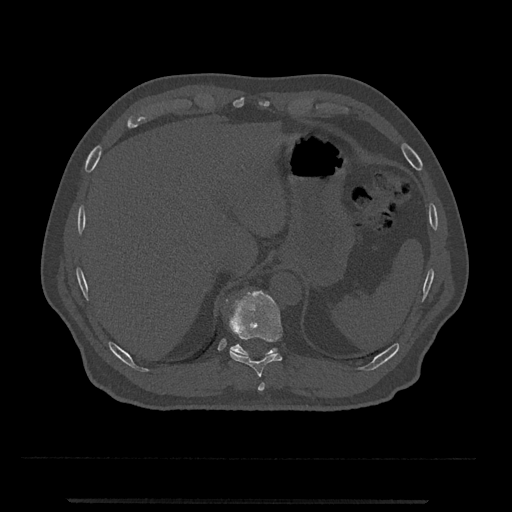
CT including the spine, one axial slice. Slice 504 of 797 in the series (ordered by position). Bone window (W 1800 / L 400 HU). 0.5 mm slice thickness. 512 × 512 image matrix. Male patient, age 63 years. Case-level facts recorded for this patient, not image findings: primary cancer: prostate.
Outlined on this slice (semi-automatic segmentation, software-assisted and operator-edited):
- T10 vertebra: bounding box [x1, y1, x2, y2] px = [226, 291, 283, 378]
- T11 vertebra: [230, 344, 278, 357]
- T9 vertebra: [258, 383, 265, 391]